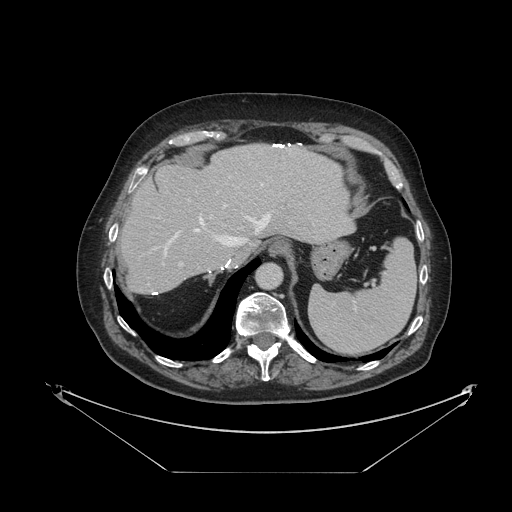
Contrast-enhanced abdominal CT, one axial slice; slice 87 of 121 in the series (ordered by position); reconstruction kernel STANDARD; 120 kVp; intravenous contrast given; soft-tissue window (W 400 / L 40 HU); 2.5 mm slice thickness; 512 × 512 image matrix. Male patient, age 68 years. Case-level facts recorded for this patient, not image findings: diagnosis: colorectal cancer liver metastases, imaged before liver resection.
Annotated regions visible in this slice (manually delineated by an expert):
- hepatic veins: box from (x=163, y=184) to (x=270, y=253) px
- liver: (x=121, y=144)–(x=353, y=294)
- planned liver remnant (the part of the liver to remain after resection): (x=121, y=144)–(x=353, y=294)
- portal vein (with intrahepatic branches): (x=179, y=204)–(x=227, y=266)